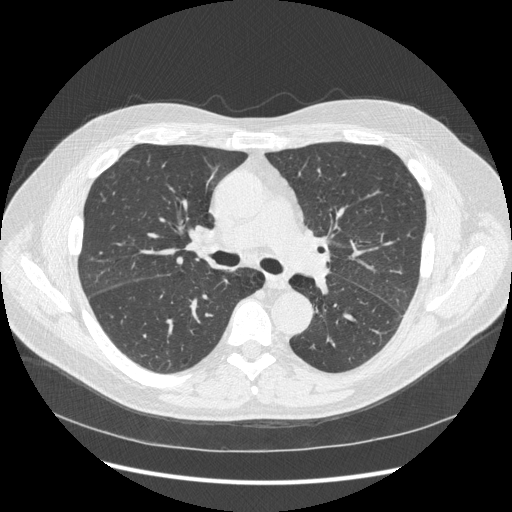
Chest CT (low-dose screening protocol), one axial image. Second annual screen. Lung window (W 1500 / L -600 HU). 1.25 mm slice thickness. 120 kVp. Male, age 59 years at enrolment. Current smoker at enrolment.
- Expert reader's lesion annotation, box from (x=182, y=217) to (x=235, y=256) px.
- Reader record for this screening exam (exam-level; its link to the box is not recorded): non-calcified nodule or mass ≥4 mm, lingula, 5 × 5 mm, smooth margins, soft tissue attenuation, pre-existing on the prior screen: yes; interval growth: no.
- Note: the box lies in the patient's right hemithorax on this image, whereas the reader's record names the left lung; they may be different findings.
- Later outcome: lung cancer diagnosed 540 days after this screen (after the third annual screen) — squamous cell carcinoma, keratinizing, NOS, right hilum, stage IIIB (AJCC 6th edition).